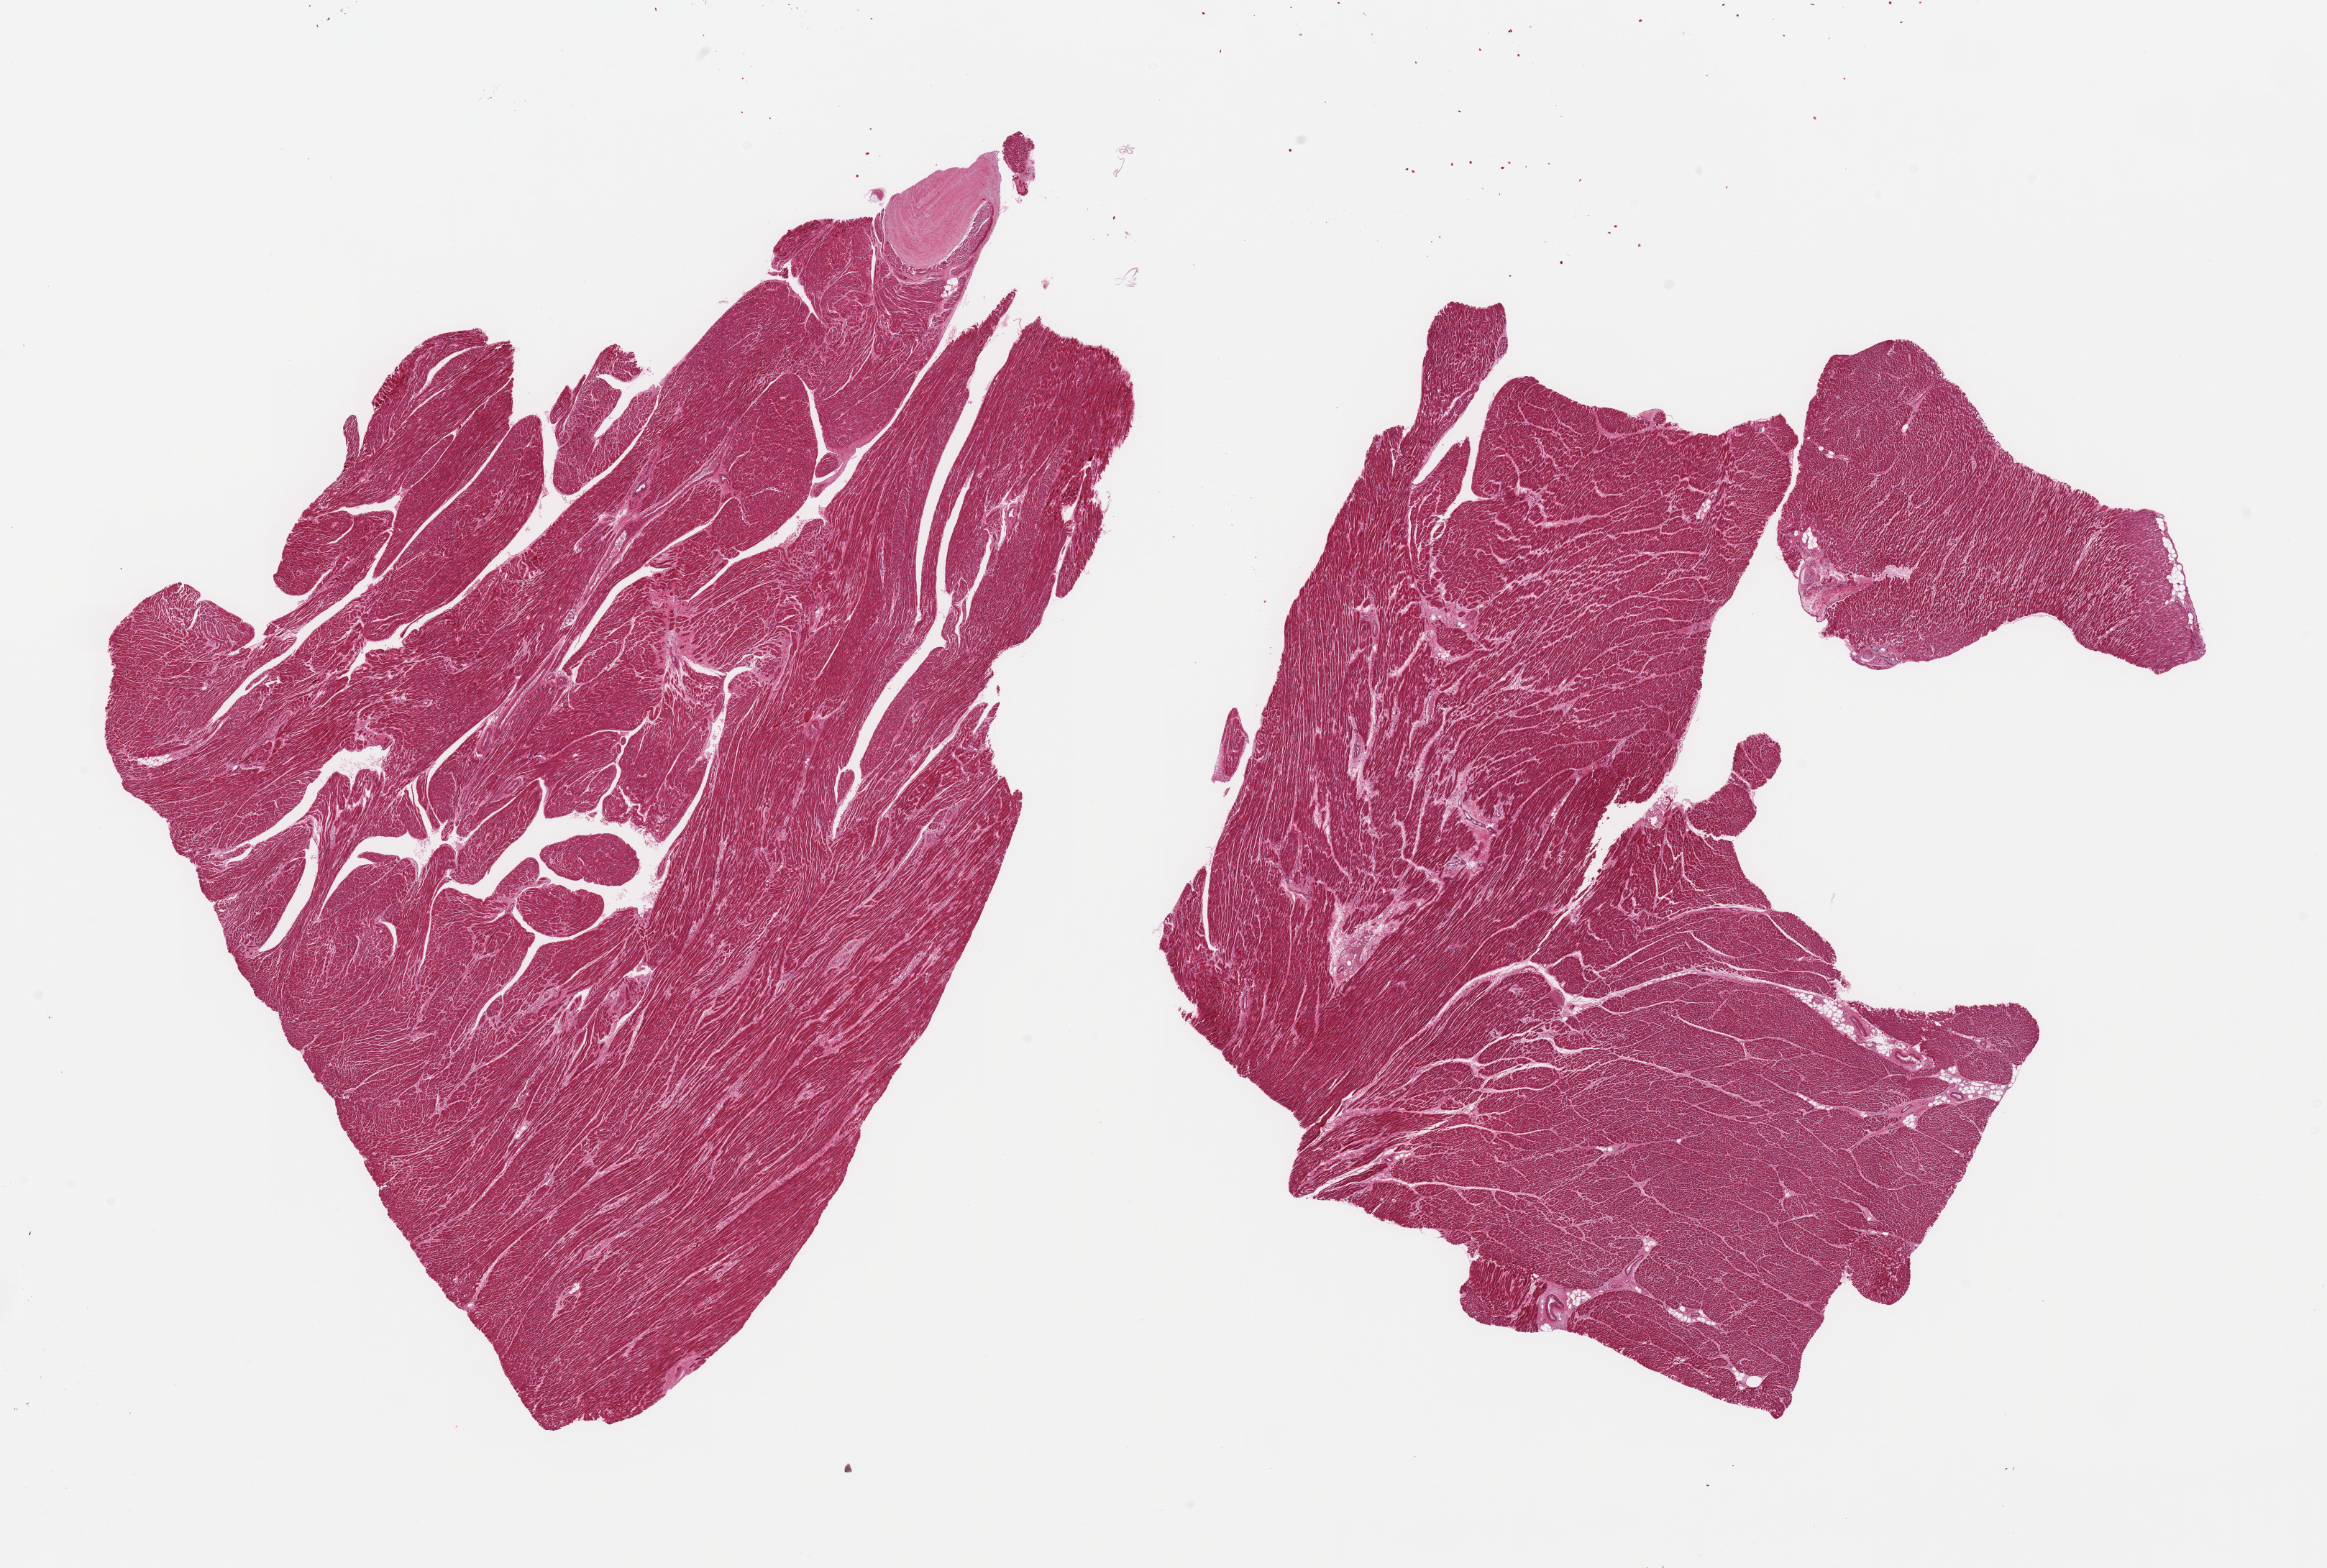
Hematoxylin and eosin (H&E) whole-slide image, brightfield — low-resolution overview of the scanned area, about 25.6 x 17.3 mm; PAXgene-fixed, paraffin-embedded tissue; target tissue: heart; donor tissue sample.
Pathologist's review note for this sample: 2 pieces; scattered enlarged myofibers; slight increase of interstitial fibrous tissue.